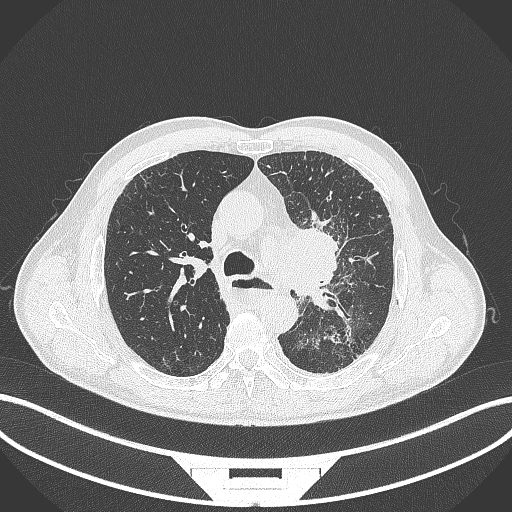
Chest CT, one axial slice; position 259 of 411 along the scan axis; reconstruction kernel B70f; lung window (W 1500 / L -600 HU); 1 mm slice thickness; 512 × 512 image matrix. Patient: male, 57 years. Case-level facts recorded for this patient, not image findings: clinical TNM (as recorded): T2a N1 M0.
Structures marked on this image (bounding box drawn by a radiologist):
- lung tumour (recorded histology: squamous cell carcinoma): bounding box [x1, y1, x2, y2] px = [294, 227, 354, 301]